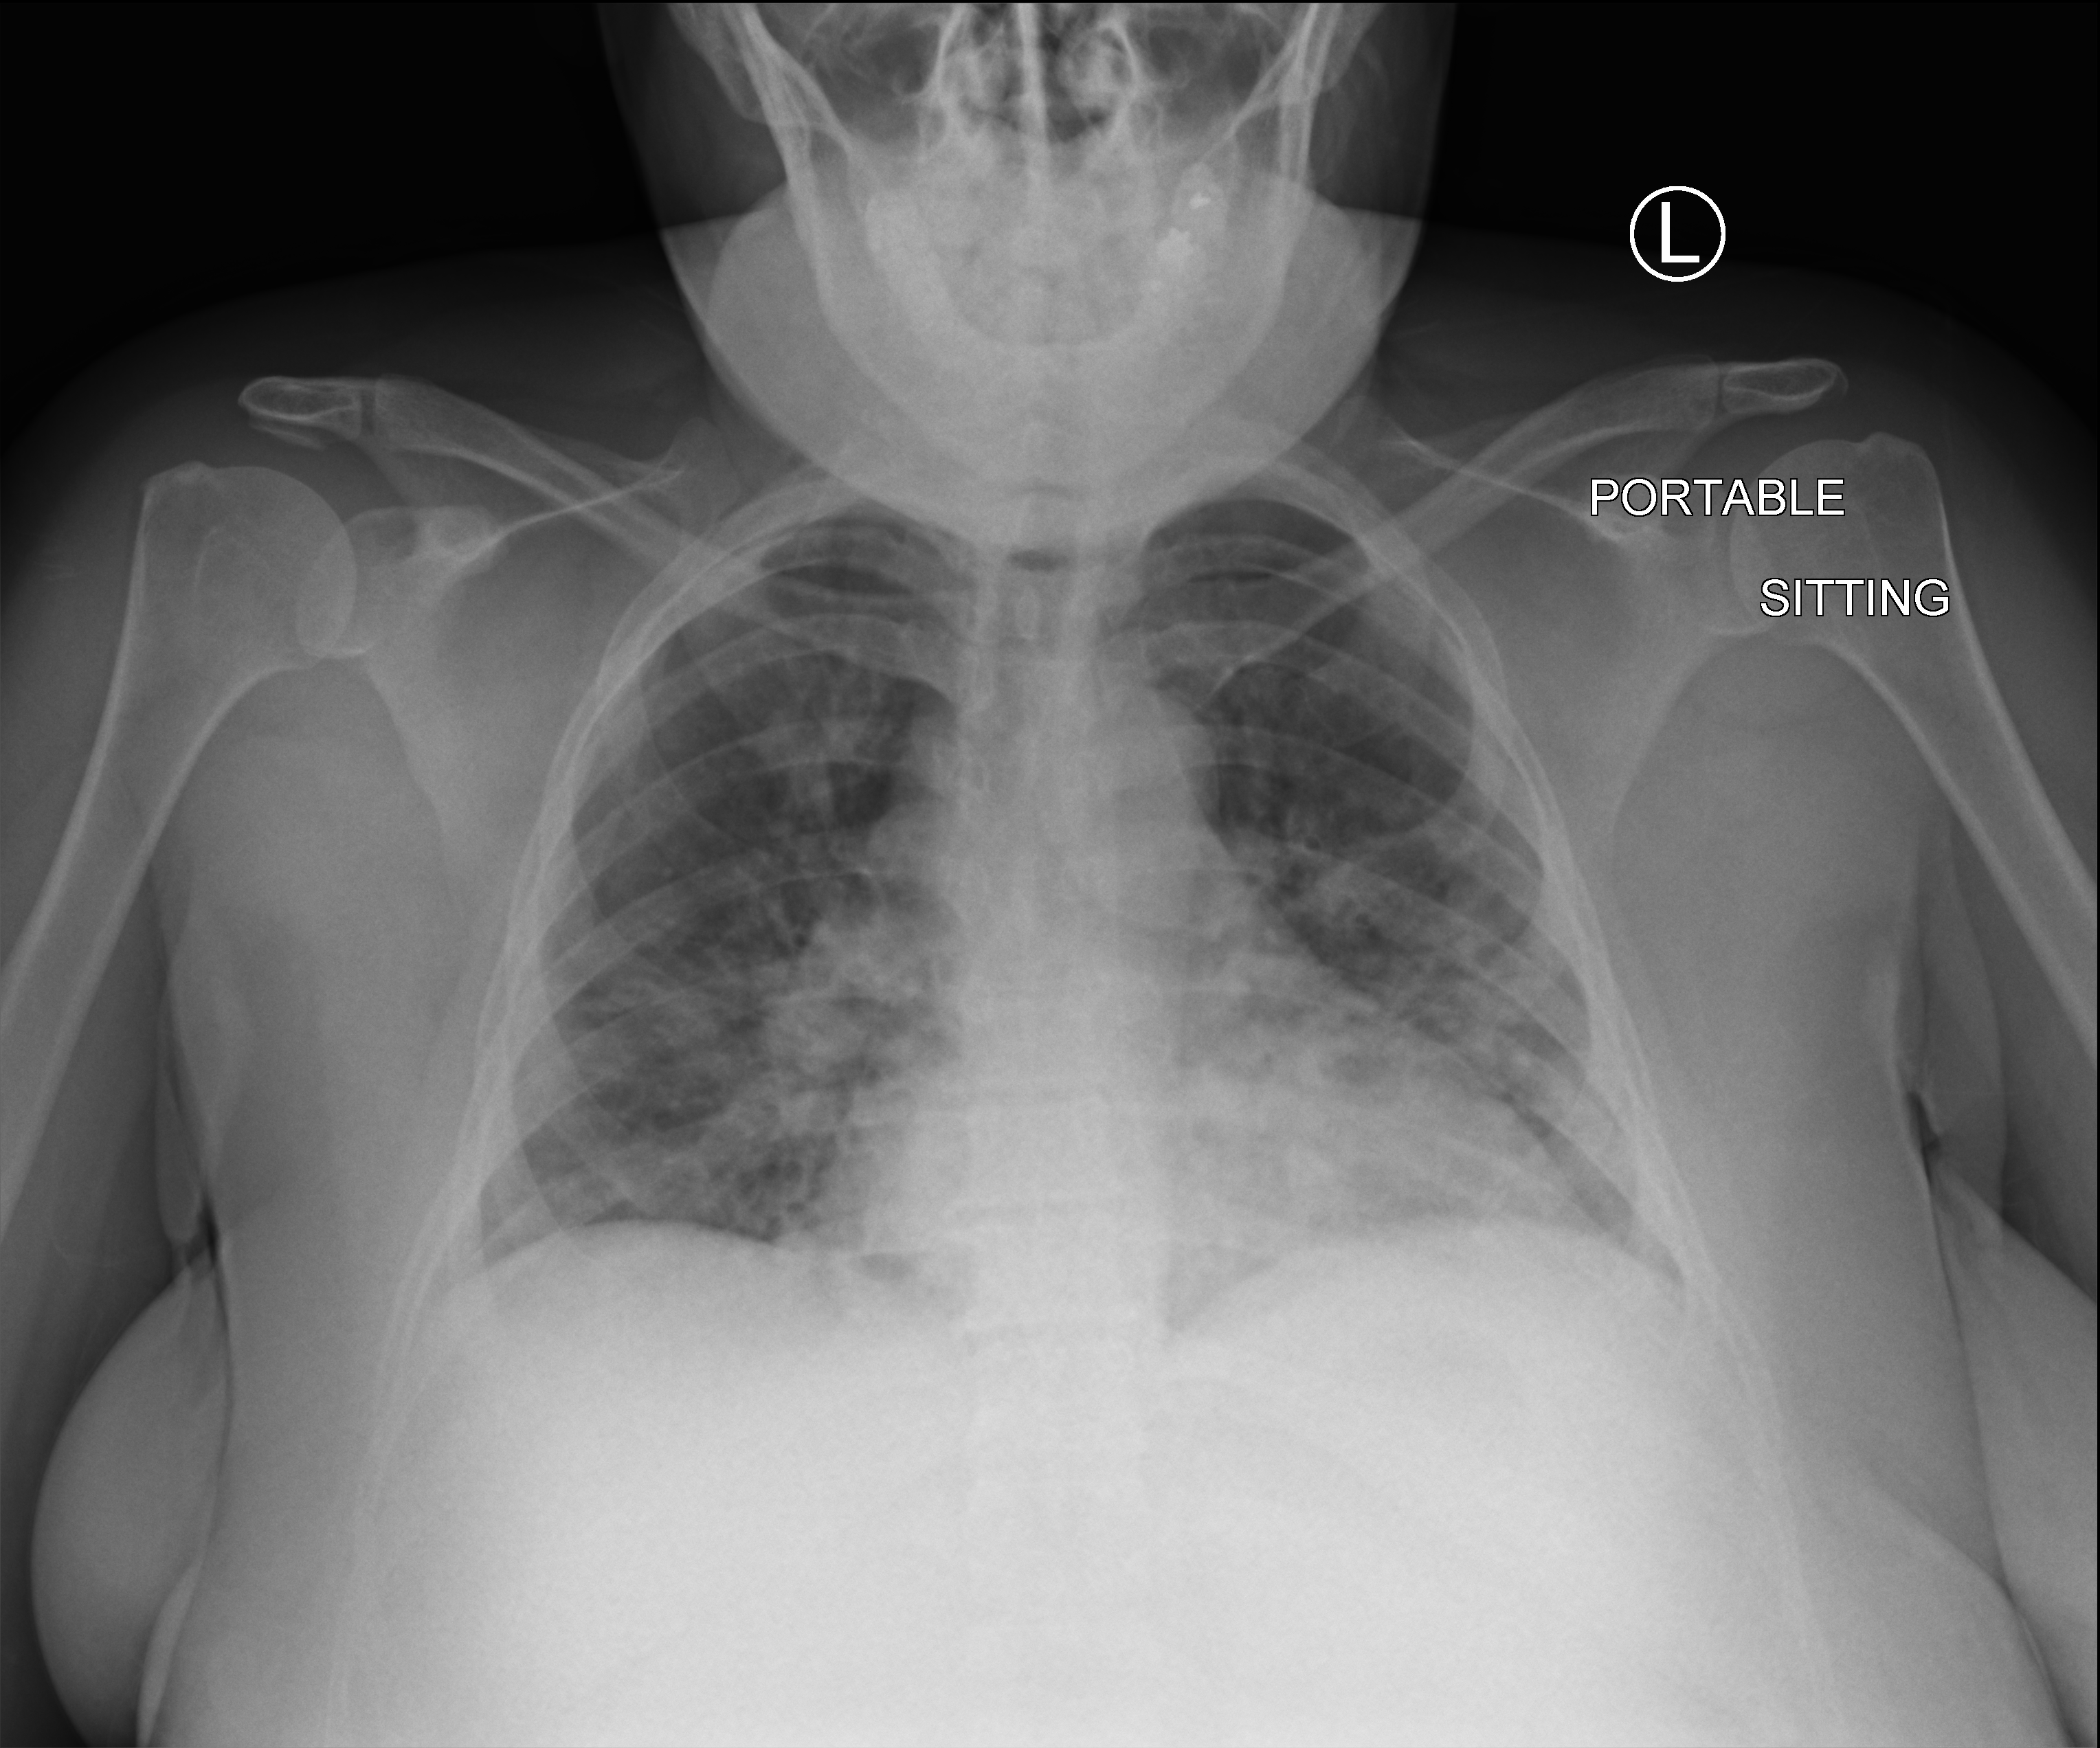
Portable chest radiograph; anteroposterior (AP) projection. Female patient hospitalised with COVID-19, age 18–59 years.
Hospital-stay facts (about this admission, not read from this image; timing relative to this image not recorded):
- diabetes (admission record): yes
- mechanically ventilated during this hospital stay: yes